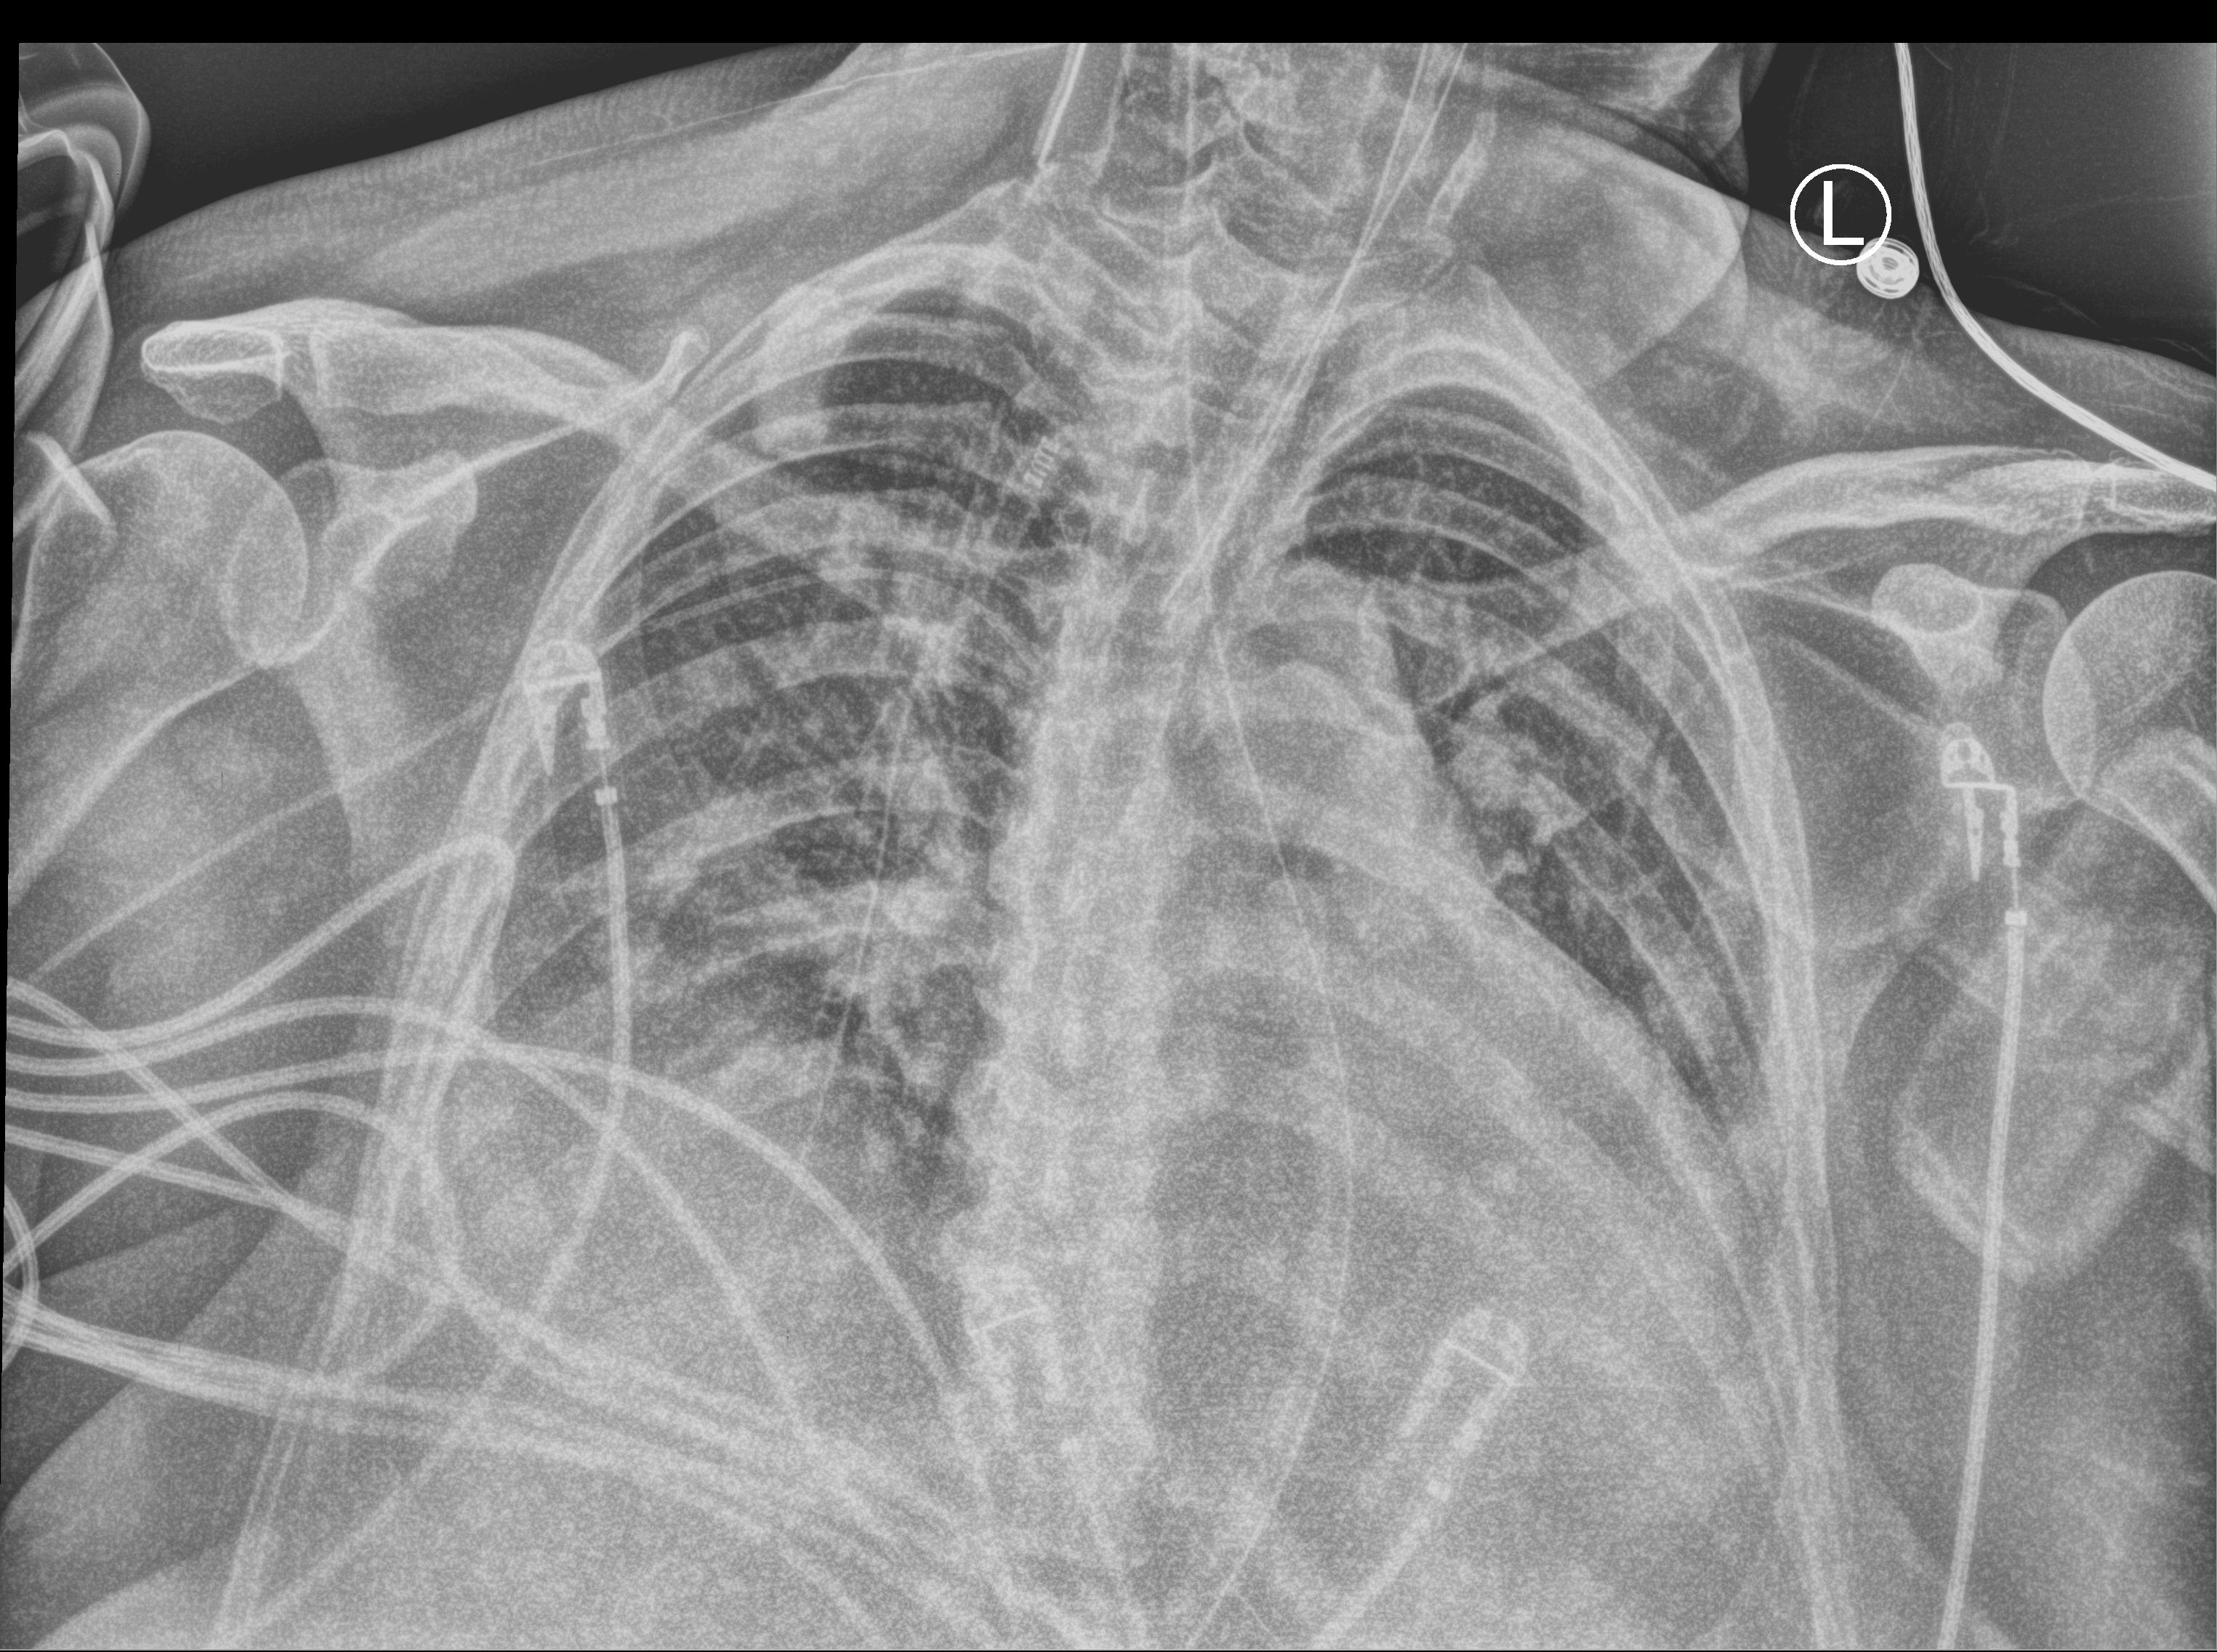
Portable chest radiograph, anteroposterior (AP) projection. Patient hospitalised with COVID-19; female, aged 60–74 years.
Admission-level facts for this patient (not findings on this image; timing relative to this image not recorded): admitted to intensive care during this hospital stay: yes.